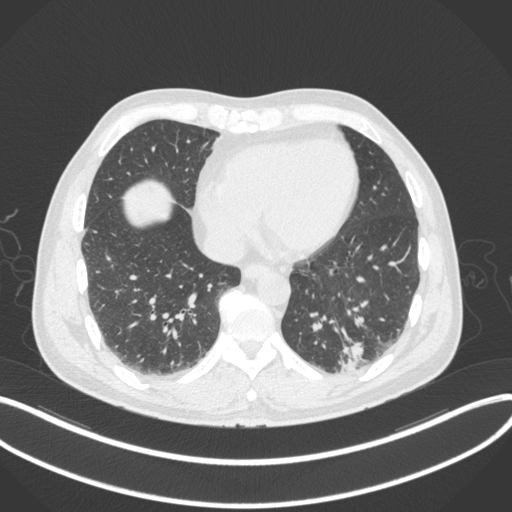
Chest CT, one axial slice. Position 89 of 313 along the scan axis. Reconstruction kernel B31f. Lung window (W 1500 / L -600 HU). 512 × 512 image matrix. Patient: male, 54 years. From the clinical record (not read from this slice): clinical TNM (as recorded): T1c N0 M1; histopathological grade: G3.
Outlined on this slice (bounding box drawn by a radiologist):
- lung tumour (recorded histology: adenocarcinoma): bounding box (x1, y1, x2, y2) in pixels: (333, 337, 365, 376)